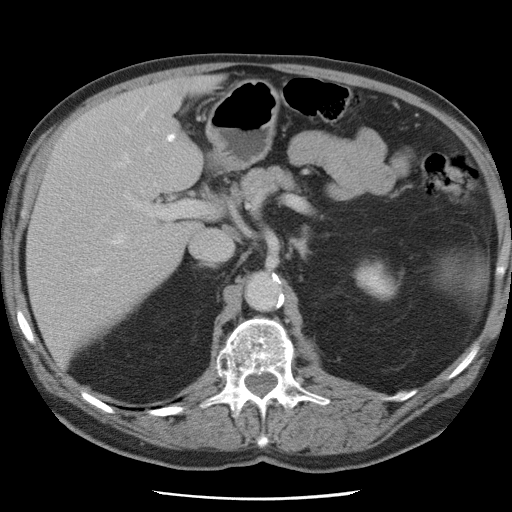
Contrast-enhanced abdominal CT, one axial slice; position 44 of 78 along the scan axis; 120 kVp; intravenous contrast given; soft-tissue window (W 400 / L 40 HU); 5 mm slice thickness; 512 × 512 image matrix. Male patient, age 75 years. Case-level facts recorded for this patient, not image findings: diagnosis: colorectal cancer liver metastases, imaged before liver resection; multiple liver metastases: yes; largest metastasis: 2.4 cm; disease in both lobes: yes.
Structures marked on this image (expert manual segmentation):
- hepatic veins: bounding box <82,110,155,282> (left, top, right, bottom; pixels)
- liver: <28,80,213,359>
- planned liver remnant (the part of the liver to remain after resection): <28,121,189,360>
- portal vein (with intrahepatic branches): <125,134,200,220>